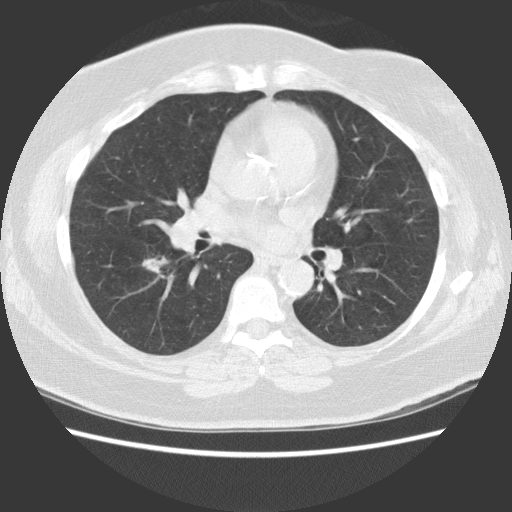
Axial slice from a low-dose chest CT screening exam, first (baseline) screen, lung window (W 1500 / L -600 HU), 2.5 mm slice thickness, standard (soft-tissue) reconstruction kernel (STANDARD), slice 59 of 117 in the series, 512 × 512 image matrix. Female participant, aged 62 years at enrolment. Former smoker at enrolment.
• Lesion marked by an expert reader, bounding box <123,240,188,294> (left, top, right, bottom; pixels).
• The exam's reader record, not a measurement of the box and not confirmed to be the same lesion: non-calcified nodule or mass ≥4 mm, right lower lobe, 12 × 10 mm, spiculated (stellate) margins, soft tissue attenuation.
• Lung cancer was diagnosed 182 days after this screen: large cell carcinoma, NOS, right lower lobe, moderately differentiated (G2), stage IA (AJCC 6th edition), 22 mm at pathology.